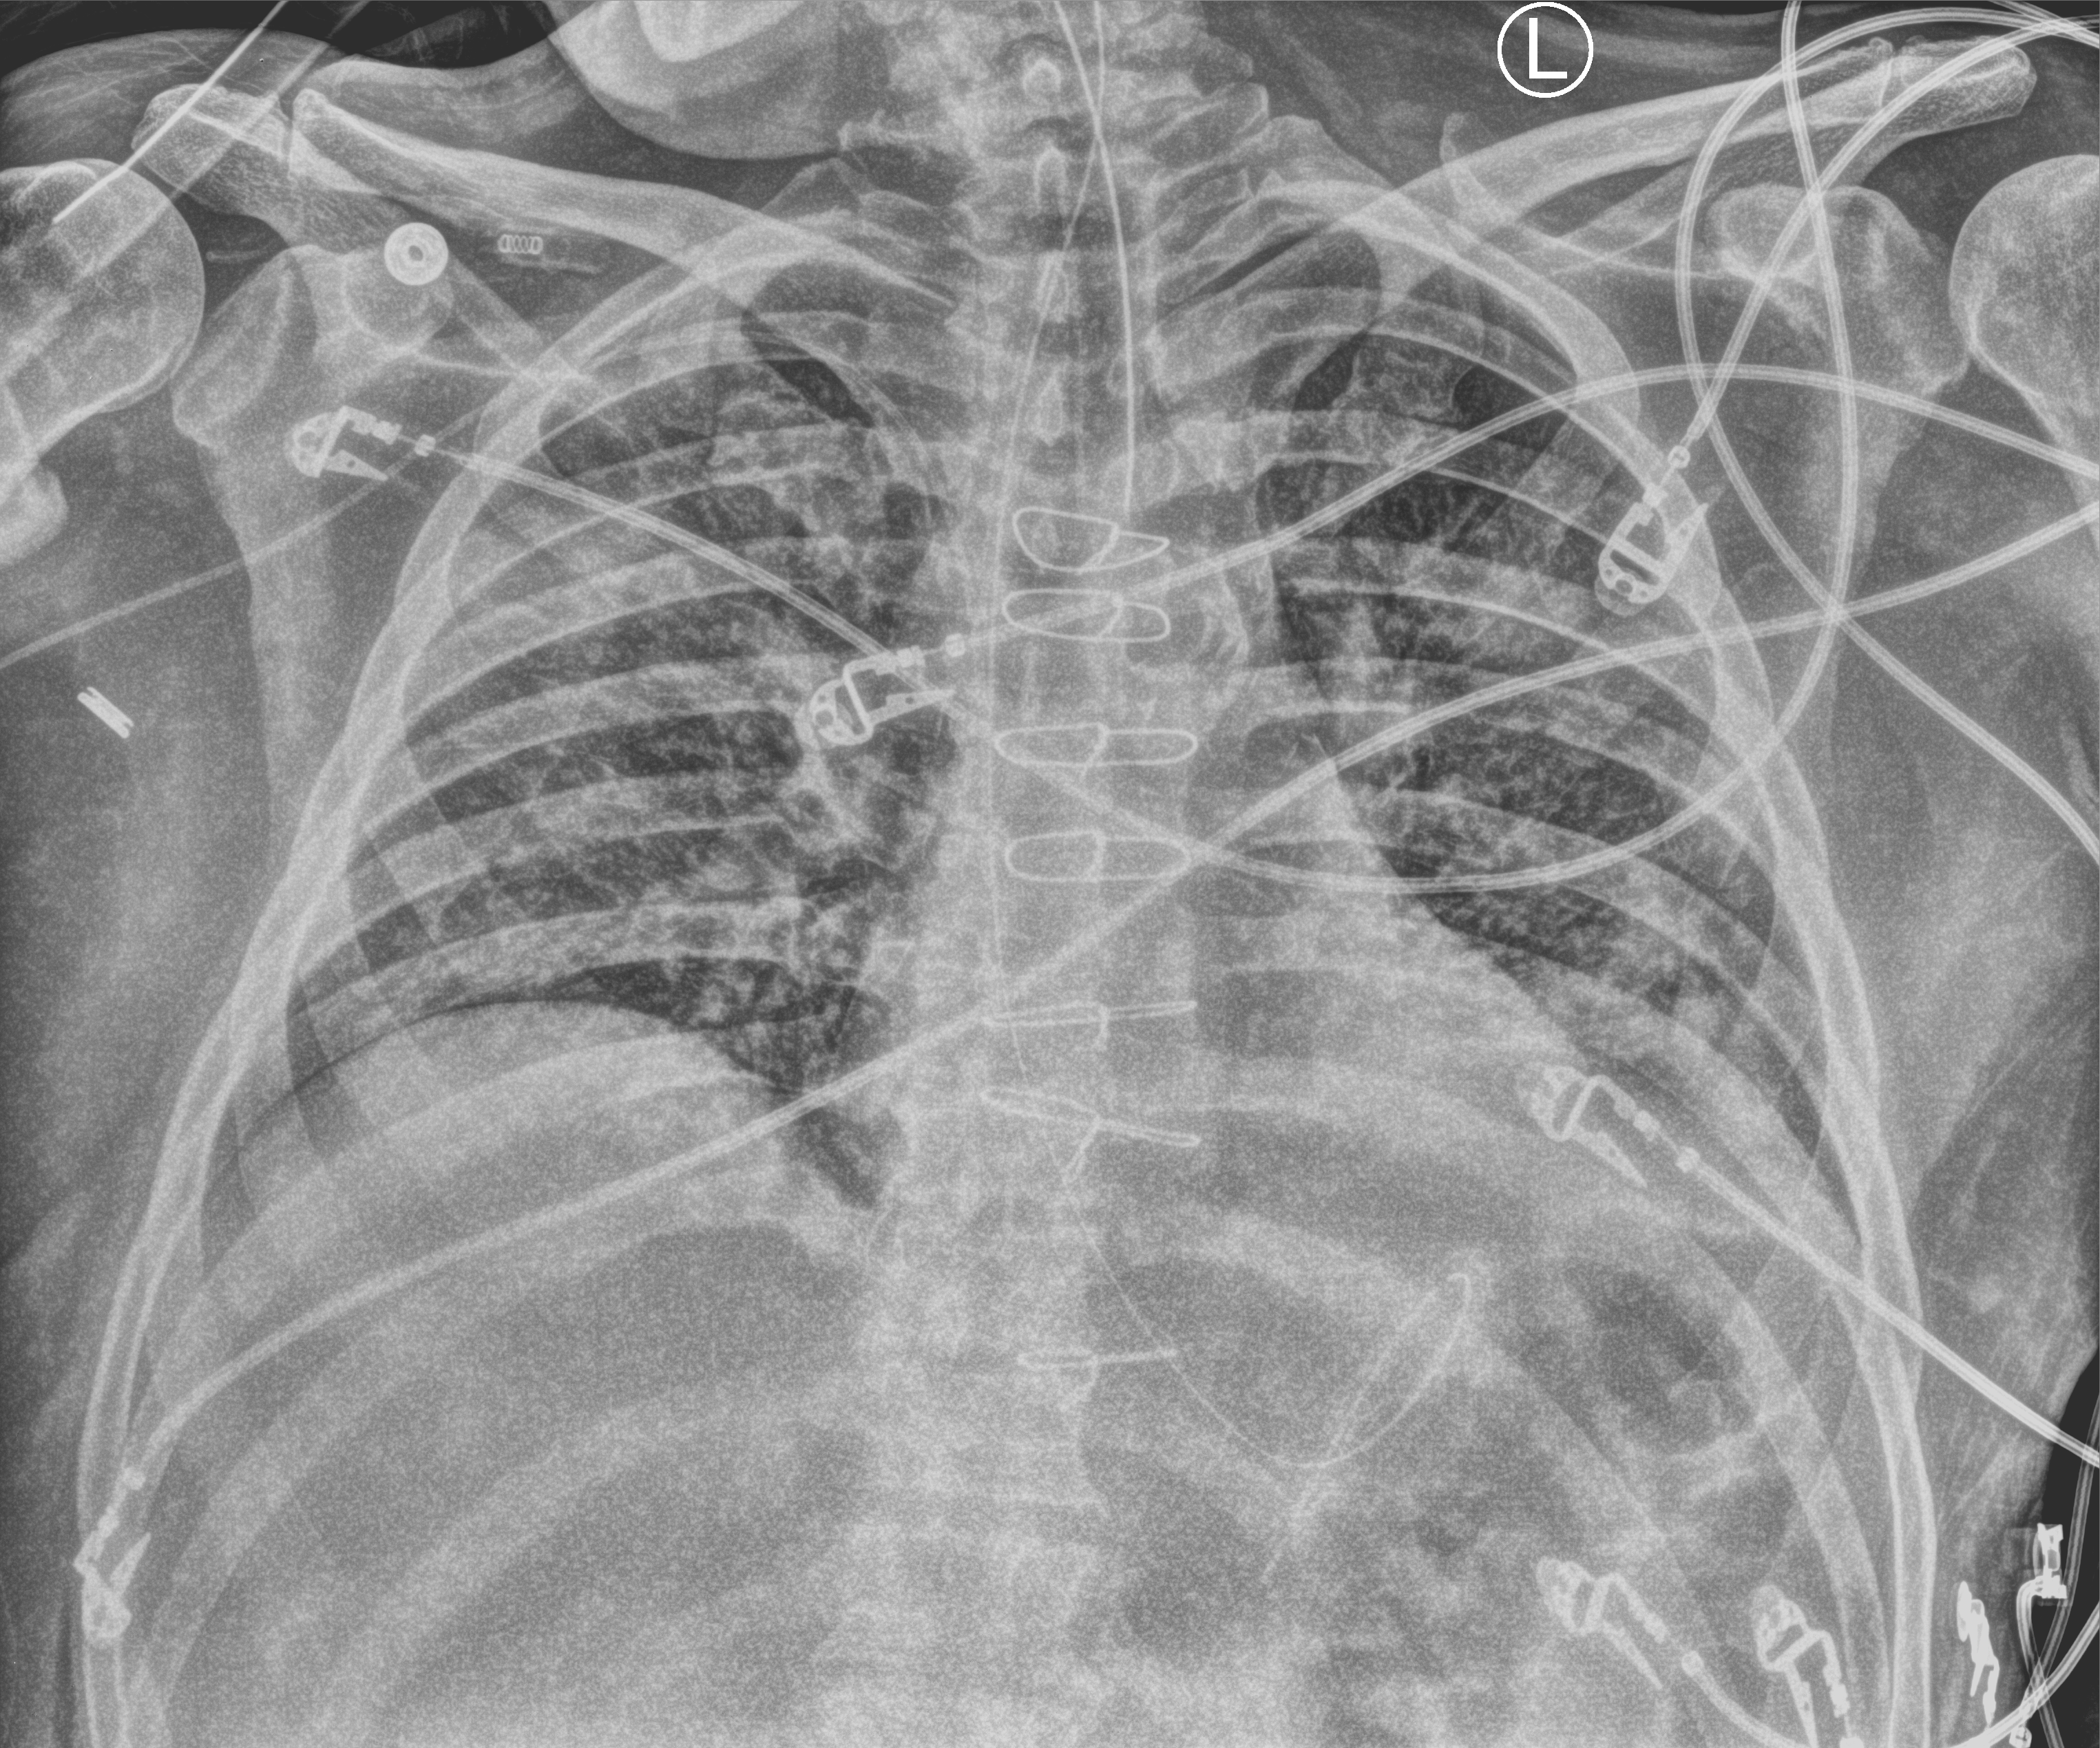
Bedside chest radiograph (computed radiography). Patient hospitalised with COVID-19; male, aged 60–74 years.
Admission-level facts for this patient (not findings on this image; timing relative to this image not recorded): other chronic lung disease (admission record): no.